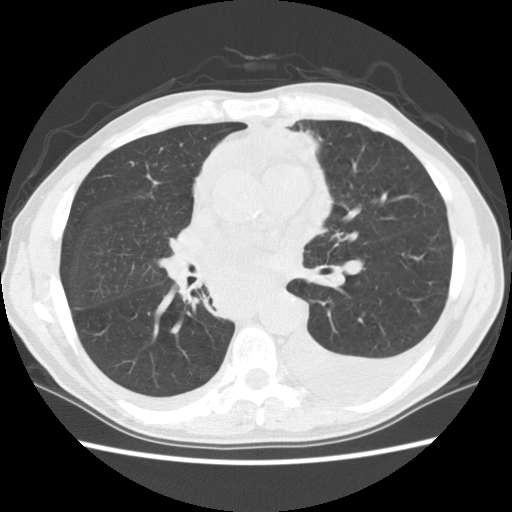
Axial slice from a low-dose chest CT screening exam; first (baseline) screen; lung window (W 1500 / L -600 HU); 2.5 mm slice thickness; slice 58 of 135 in the series. Male participant, aged 60 years at enrolment. Current smoker at enrolment.
- Expert-annotated lung lesion, bounding box (x1, y1, x2, y2) in pixels: (175, 240, 304, 332).
- Screening reader's record for this exam: no non-calcified nodule ≥4 mm recorded.
- Participant outcome: lung cancer diagnosed 12 days after this screen — squamous cell carcinoma, NOS, carina, poorly differentiated (G3), stage IV (AJCC 6th edition).